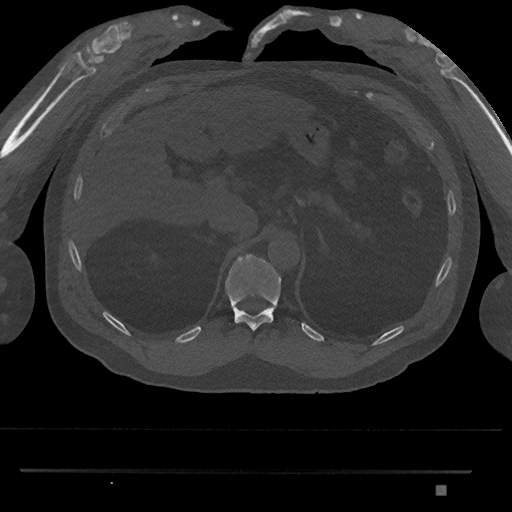
CT including the spine, one axial slice; bone window (W 1800 / L 400 HU); 0.5 mm slice thickness; 512 × 512 image matrix. Male patient, age 65 years. From the clinical record (not read from this slice): primary cancer: prostate.
Annotated regions visible in this slice (semi-automatic segmentation, software-assisted and operator-edited):
- T11 vertebra: bounding box [x1, y1, x2, y2] px = [225, 254, 282, 331]